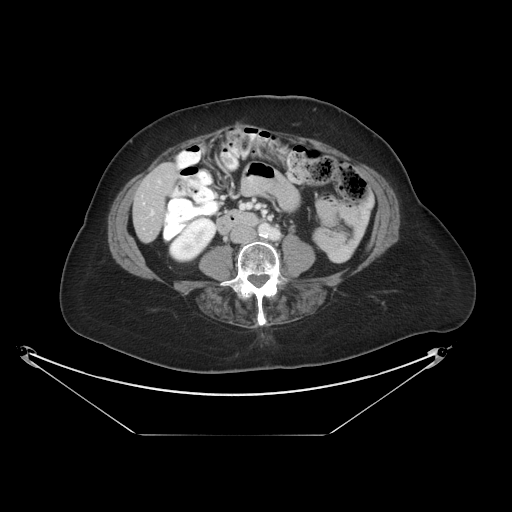
Contrast-enhanced abdominal CT, one axial slice; position 5 of 36 along the scan axis; intravenous contrast given; soft-tissue window (W 400 / L 40 HU); 5 mm slice thickness; 512 × 512 image matrix. Female patient, age 70 years. From the clinical record (not read from this slice): diagnosis: colorectal cancer liver metastases, imaged before liver resection; multiple liver metastases: no; largest metastasis: 2.5 cm; chemotherapy before resection: no.
Structures marked on this image (manually delineated by an expert):
- liver: box from (x=134, y=164) to (x=175, y=241) px